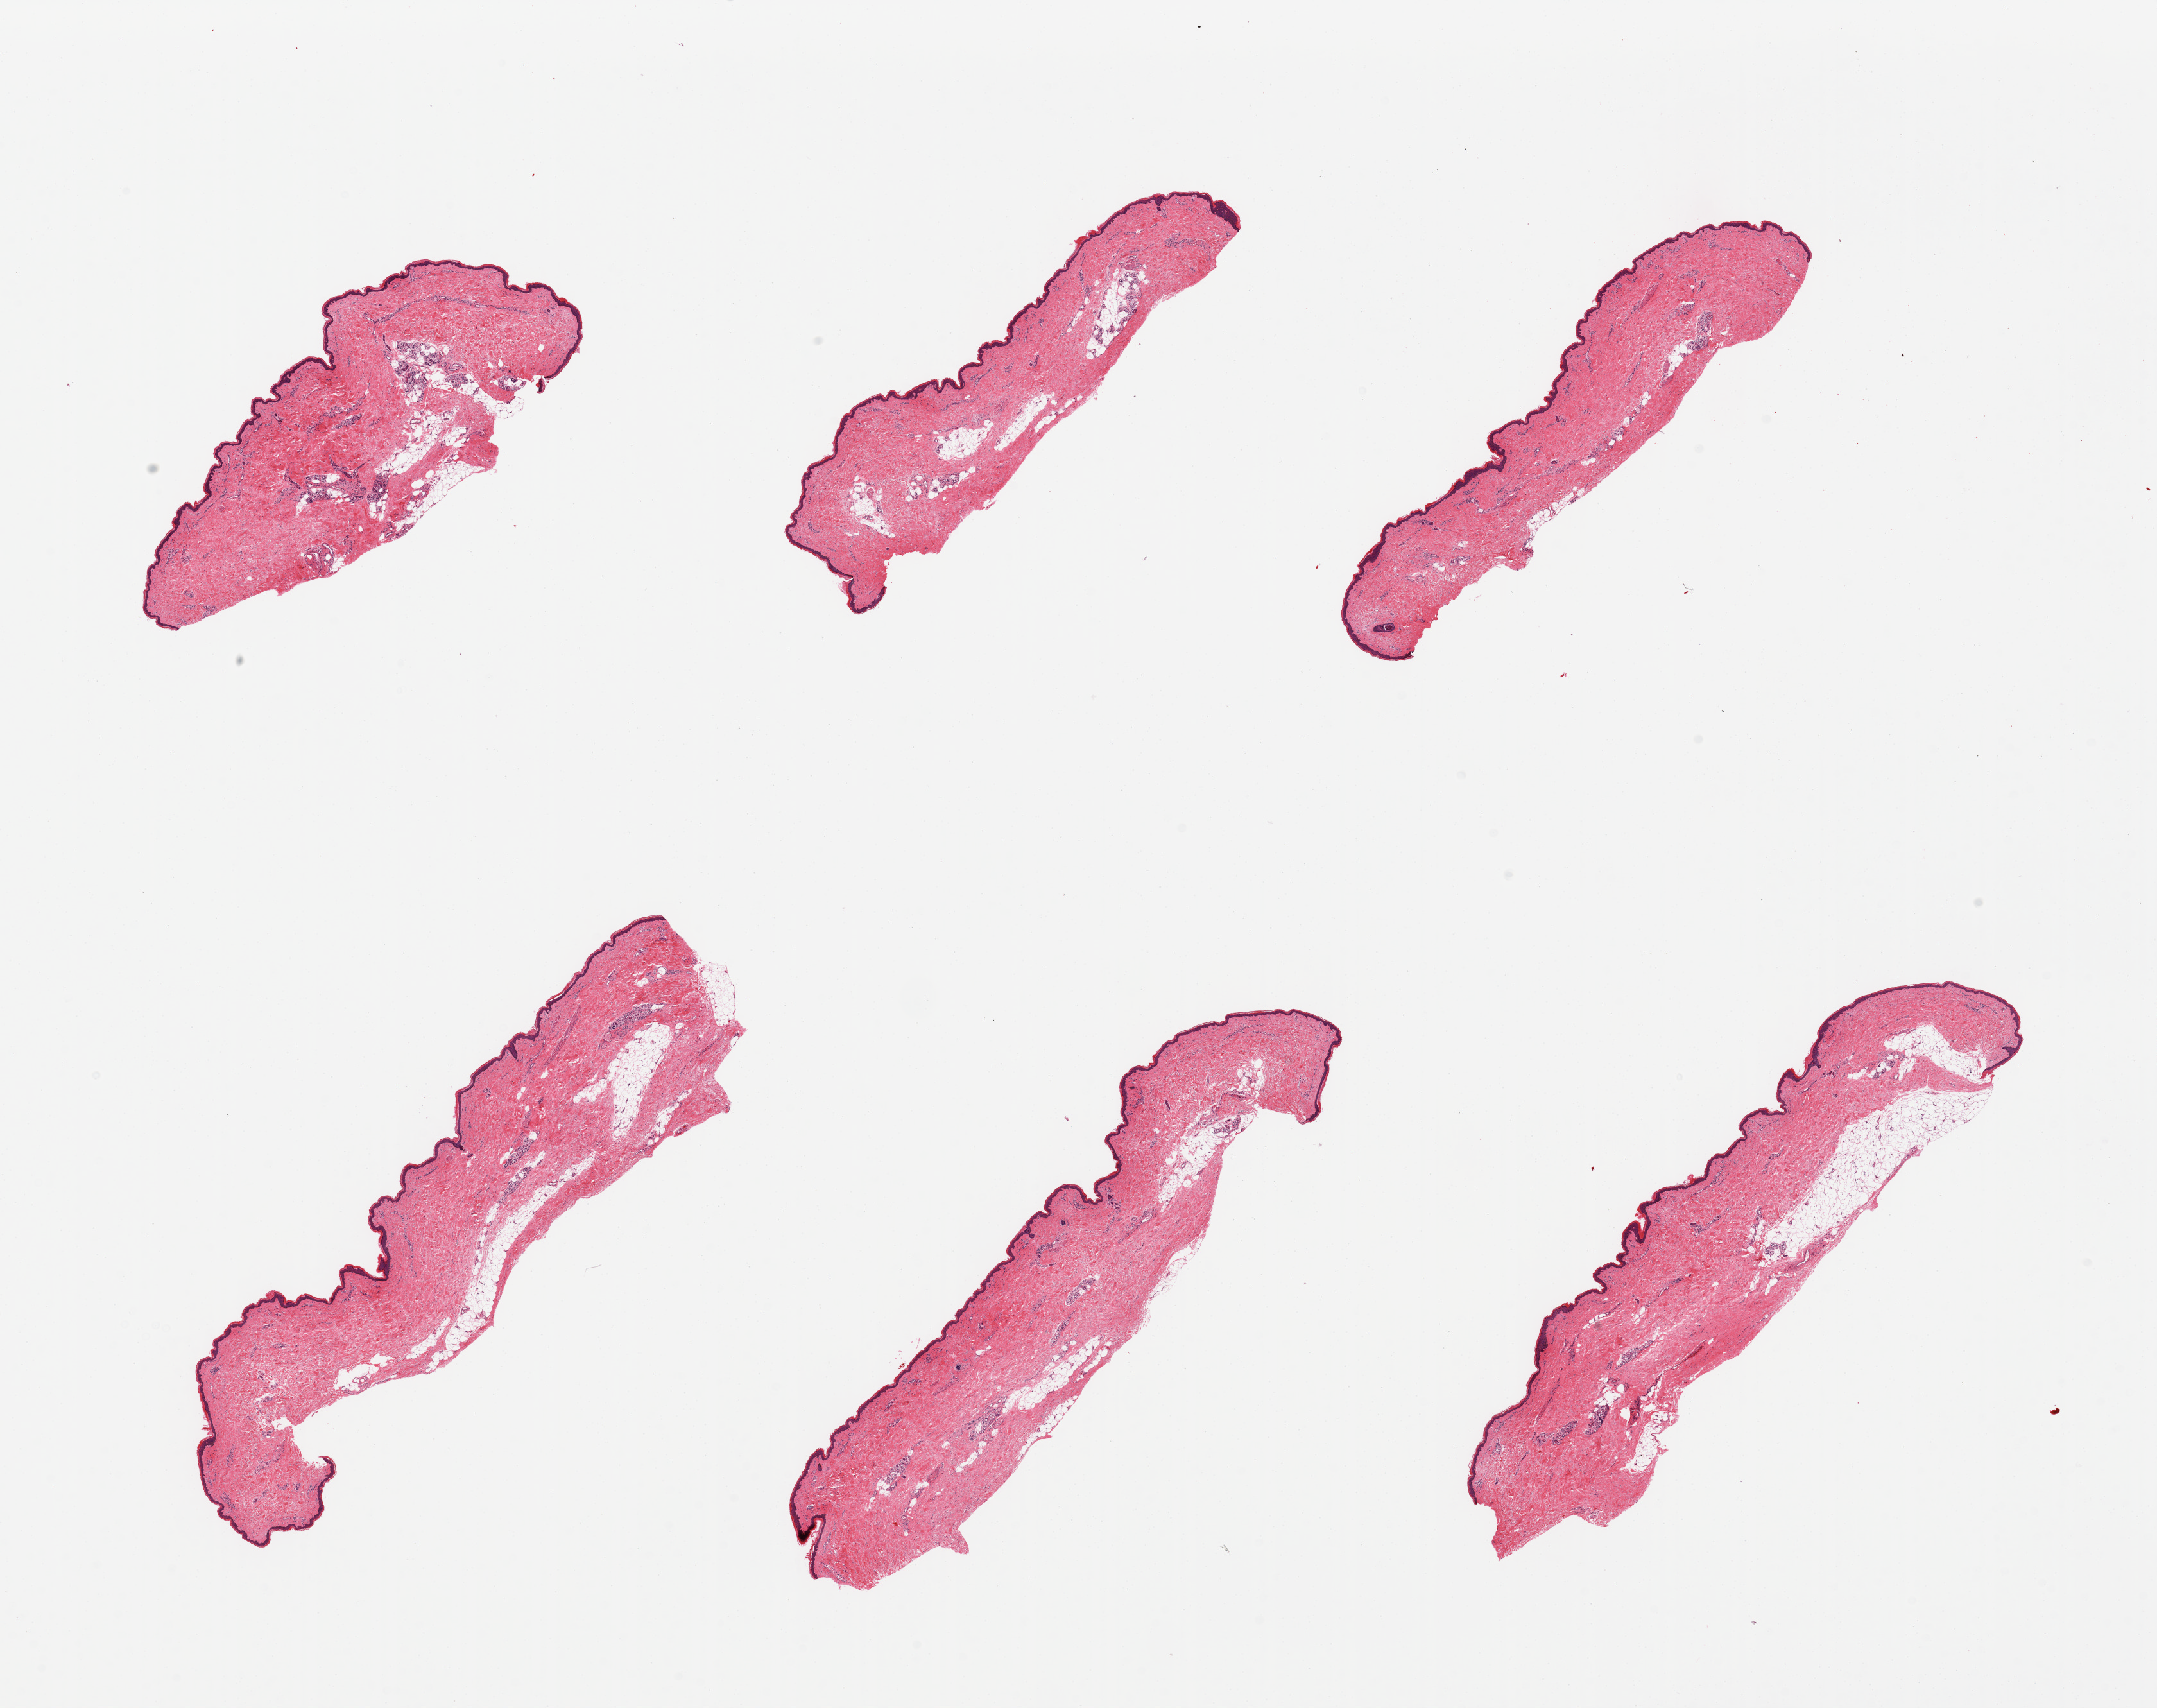
H&E whole-slide image — shown as a low-resolution overview of the whole scanned area (about 26.6 x 21.0 mm, from a 20x scan). PAXgene-fixed paraffin-embedded (PFPE) section. Sampled site (target tissue): skin of lower leg. Tissue donor sample. Male donor.
Review note (as recorded): 6 pieces, trace adherent dermal fat.